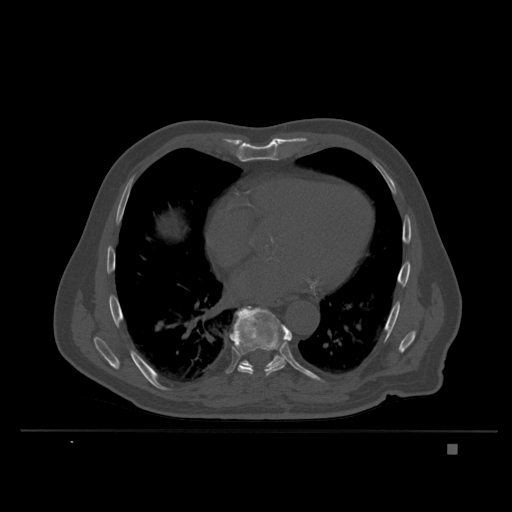
CT including the spine, one axial slice; bone window (W 1800 / L 400 HU); 1.5 mm slice thickness; 512 × 512 image matrix. Patient: male, 73 years. Case-level facts recorded for this patient, not image findings: primary cancer: skin.
Annotated regions visible in this slice (semi-automatically segmented with operator editing):
- T8 vertebra: bounding box [x1, y1, x2, y2] px = [229, 308, 293, 376]
- T9 vertebra: [236, 306, 285, 369]